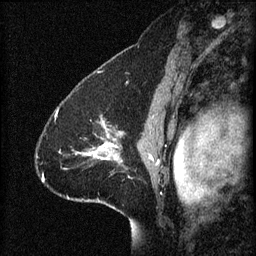
Breast MRI (dynamic contrast-enhanced), one sagittal slice. Position 45 of 60 along the scan axis. 3 images stored at this slice position (order not interpretable as contrast timing). 1.5 T. TE 4.2 ms, TR 8.2 ms. 2 mm slice thickness. 256 × 256 image matrix. Female patient, age 41 years.
Outlined on this slice (semi-automatically segmented with operator editing):
- analysis volume of interest (the breast-tissue region the enhancement analysis was run in; not a lesion): box from (x=58, y=110) to (x=123, y=169) px
- tumour enhancement mask (voxels above the 70 % enhancement threshold inside the analysis volume of interest): (x=58, y=112)–(x=120, y=161)